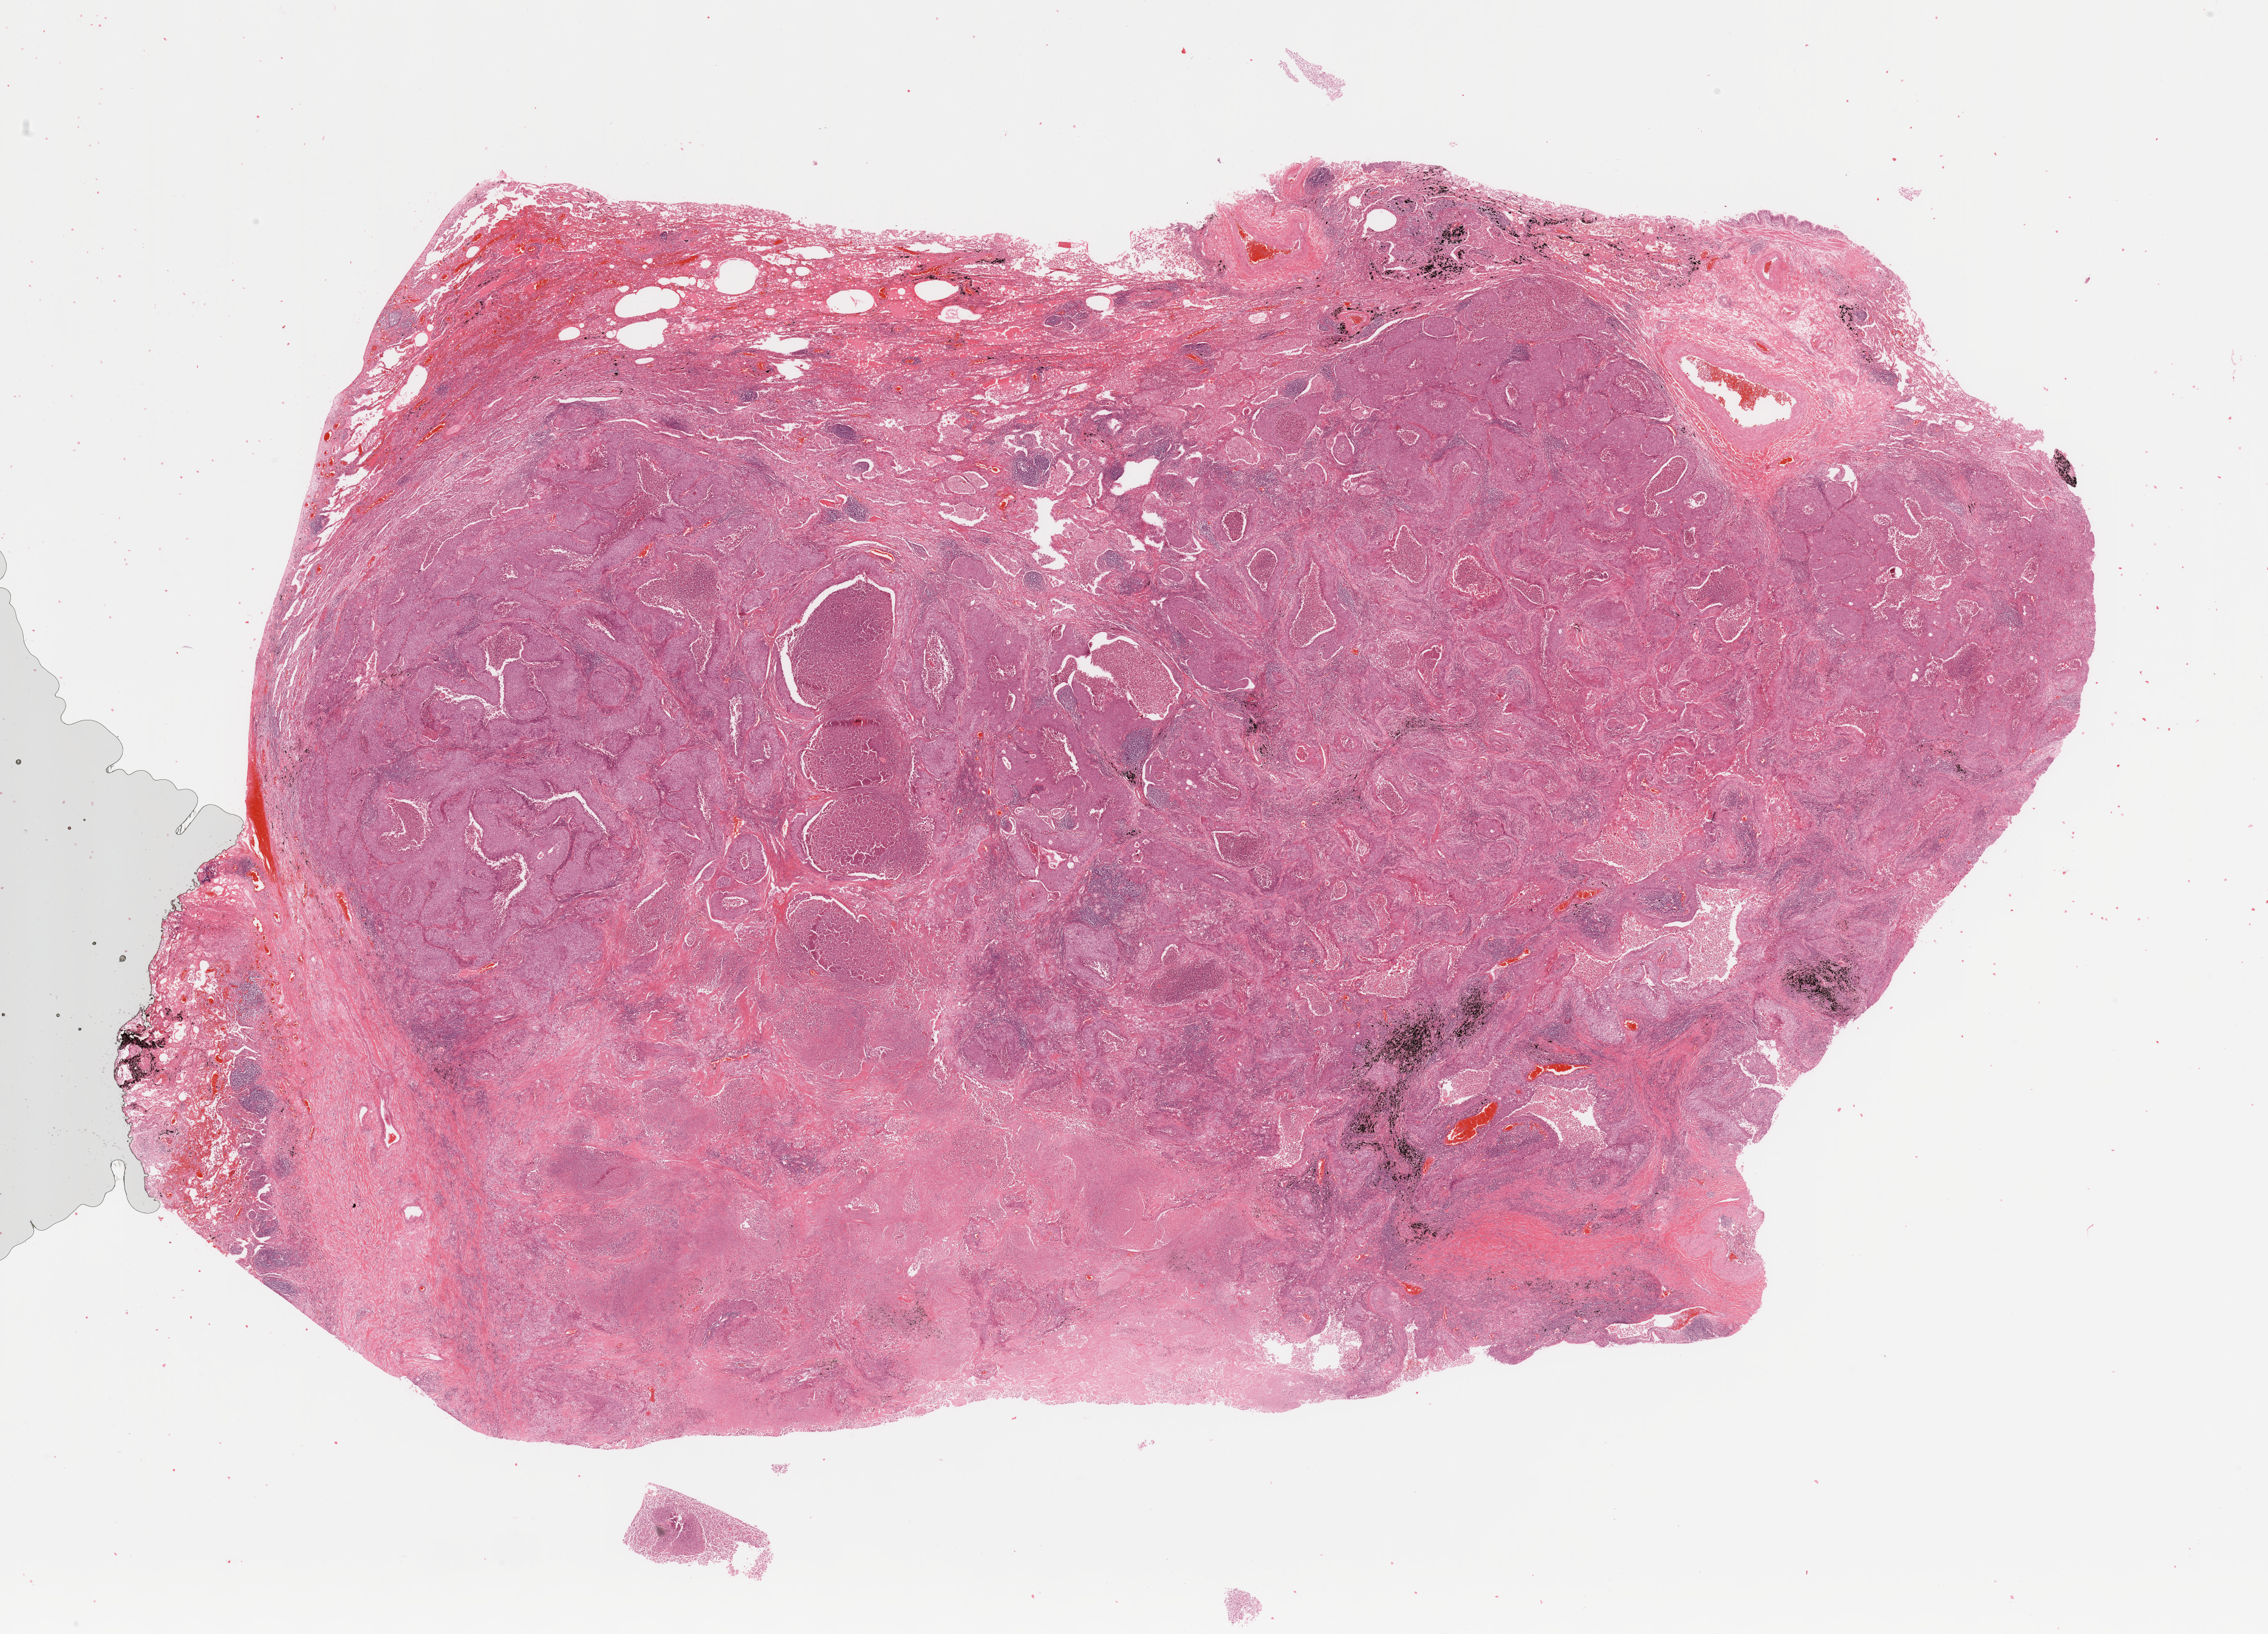
Digitized Hematoxylin and eosin (H&E) stained tissue section (whole slide) — low-resolution overview of the scanned area, about 29.5 x 21.3 mm (acquisition: 20x scan), tumour tissue sample, sampled site: lung. 72-year-old male patient. Histologic grade: G3 (poorly differentiated). Pathologist review of this section (percent, as recorded): tumour nuclei 65%, necrosis 20%.
- AJCC pathologic stage: IB
- histologic diagnosis: Squamous cell carcinoma, NOS